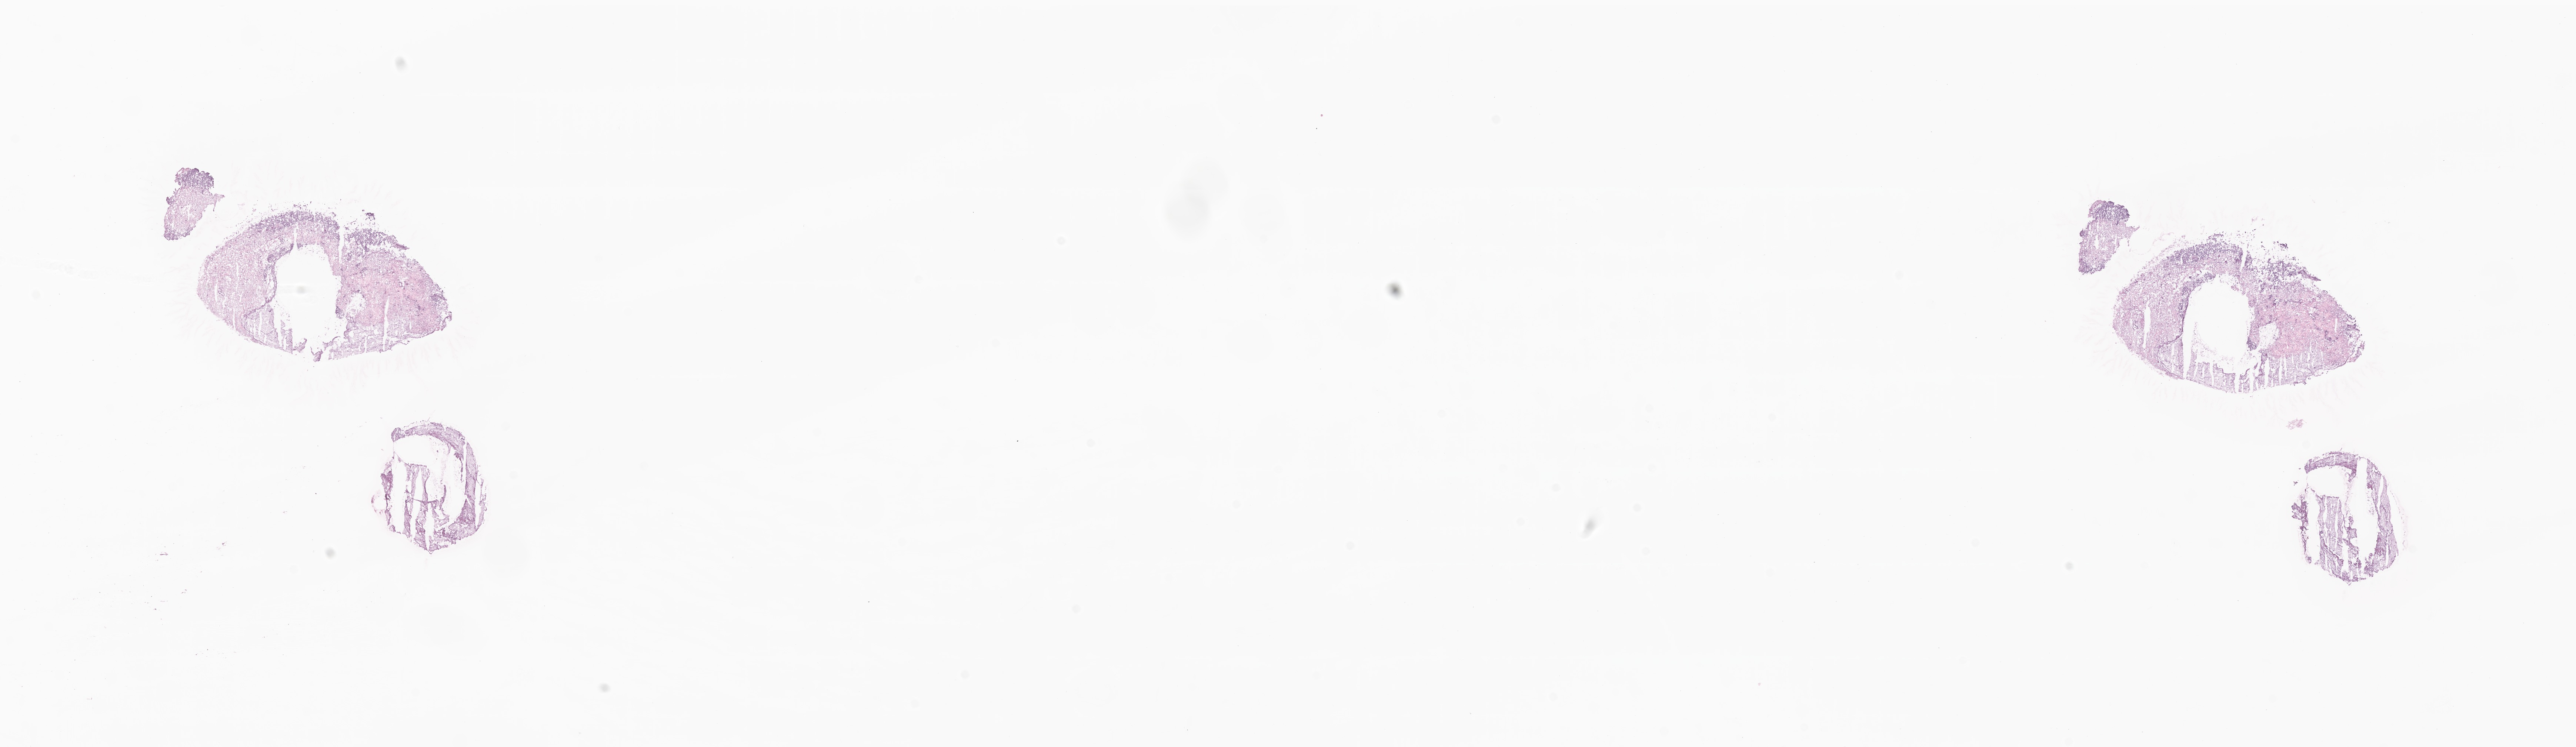
Whole-slide image, haematoxylin and eosin stain of tumor tissue from the cerebral ventricle — low-resolution overview of the scanned area, about 29.3 x 8.5 mm. Cryosection (OCT / tissue freezing medium). Female patient, age 215 months (17 years 11 months).
- diagnosis: Choroid plexus carcinoma